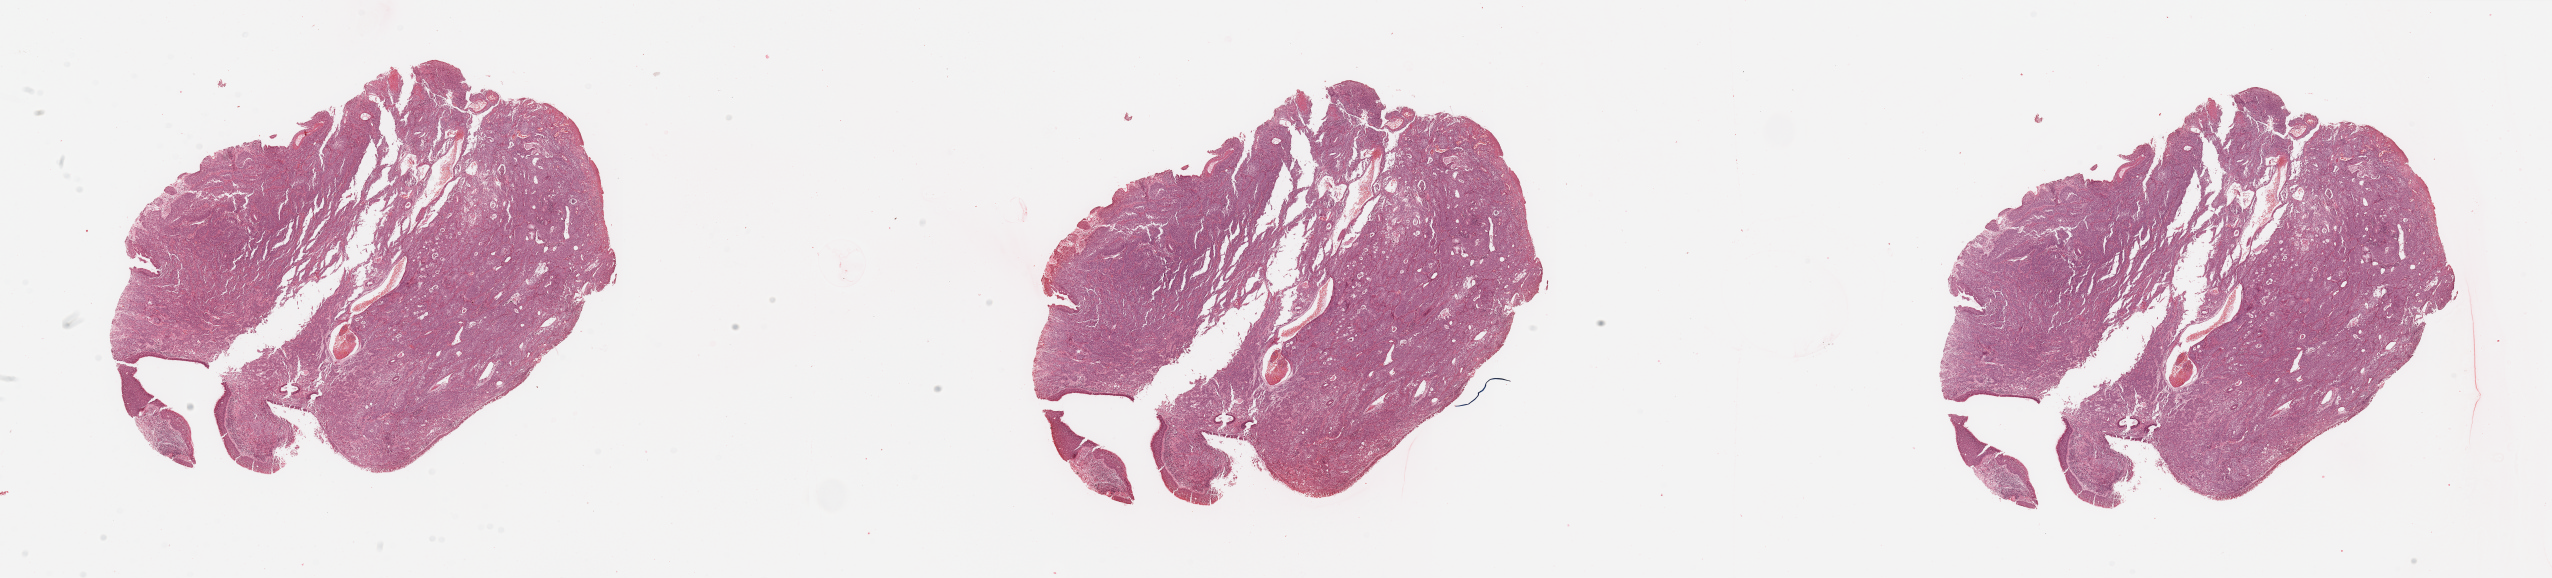
H&E-stained whole-slide image, shown as a low-resolution overview of the whole scanned area (about 40.4 x 9.1 mm, from a 20x scan), head and neck, tissue type not recorded. 60-year-old male patient.
Patient diagnosis: Squamous cell carcinoma, NOS (larynx, NOS).